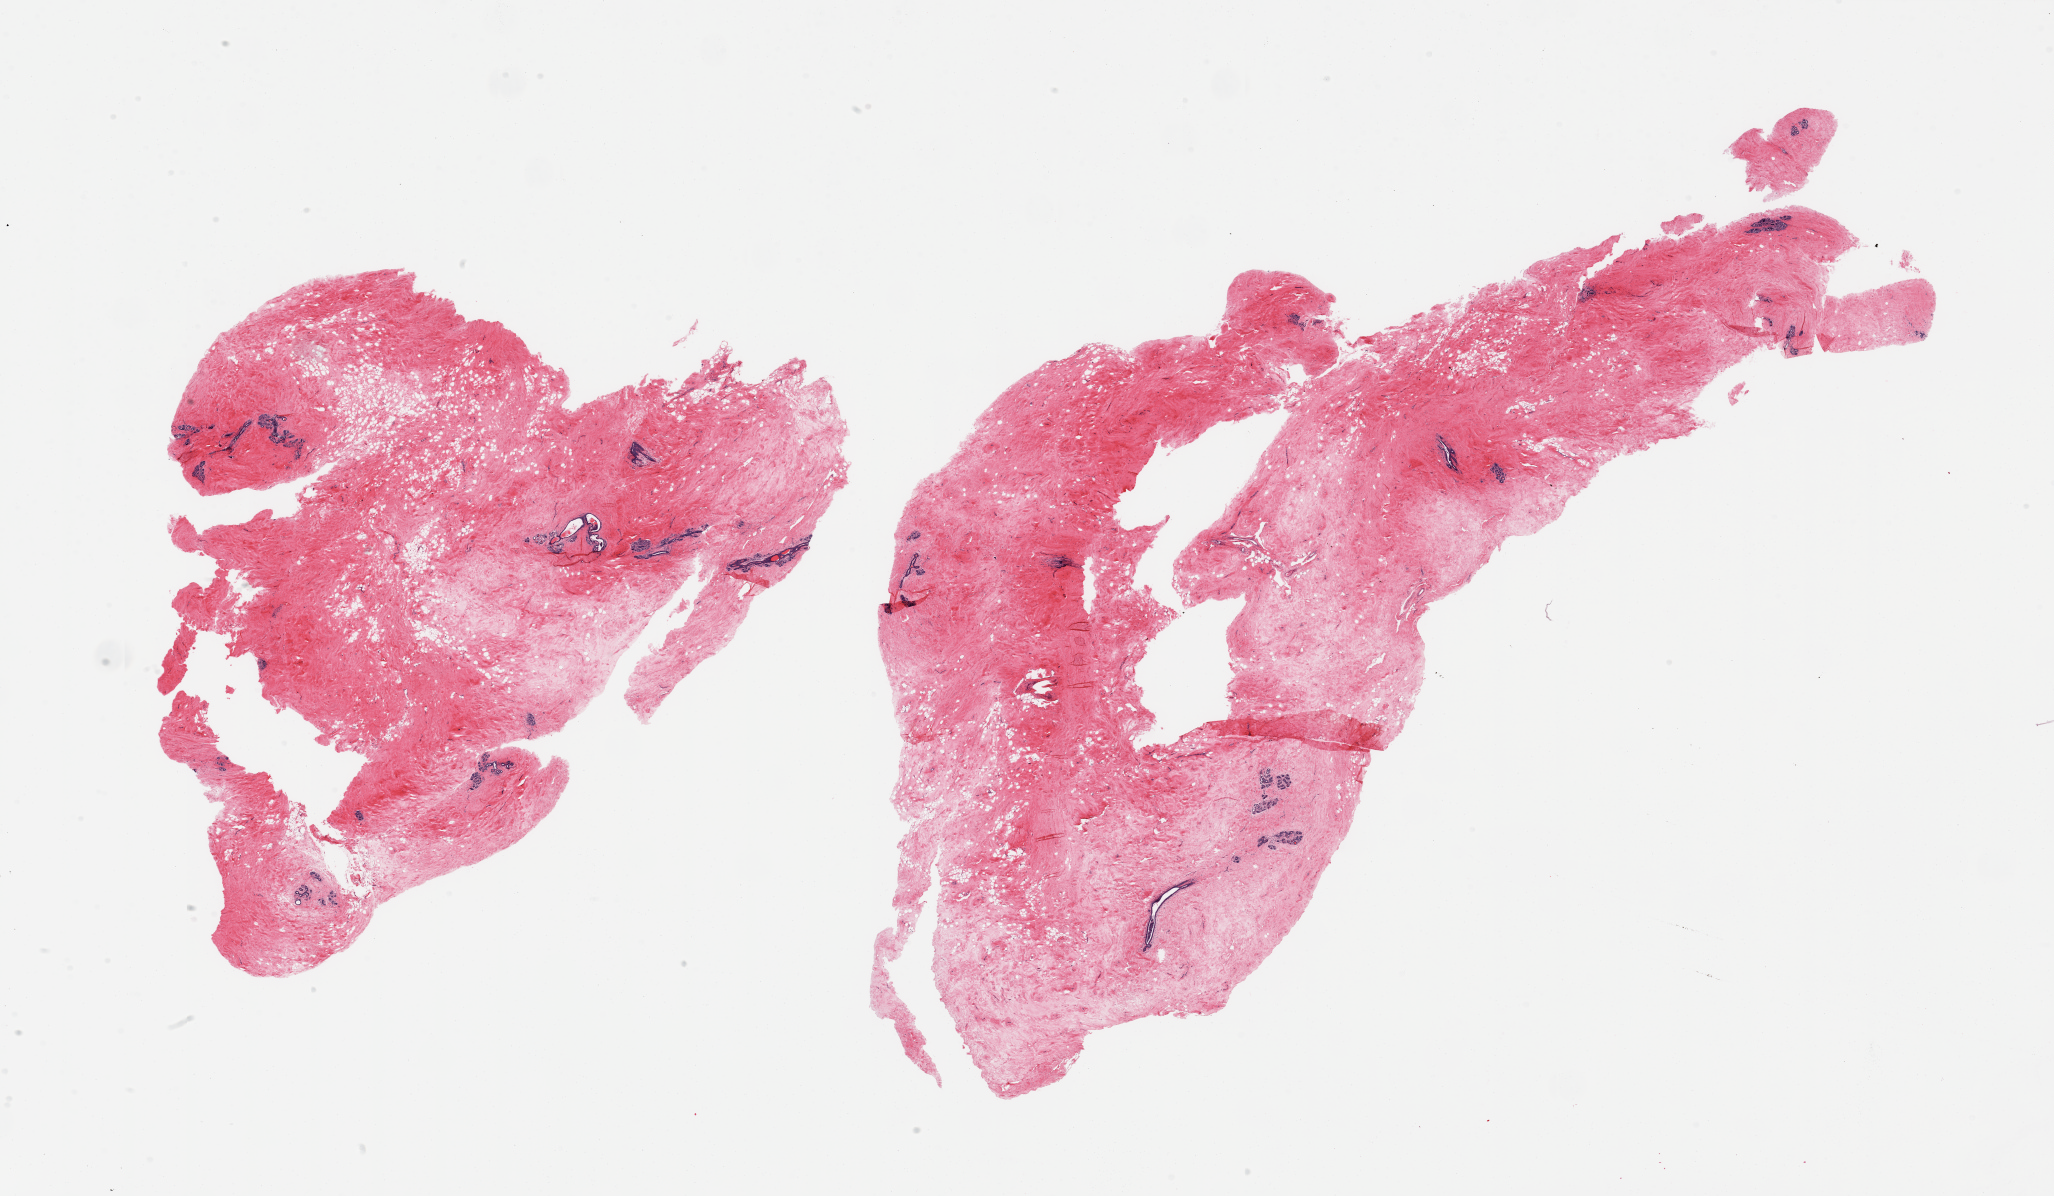
Hematoxylin and eosin (H&E) whole-slide image, brightfield — low-resolution overview of the scanned area, about 32.5 x 18.9 mm. PAXgene-fixed paraffin-embedded (PFPE) section. Section of breast (target tissue). Tissue donor sample.
Pathologist's review note for this sample: 2 pieces; atrophic ducts & lobules in mainly fibrous stroma.